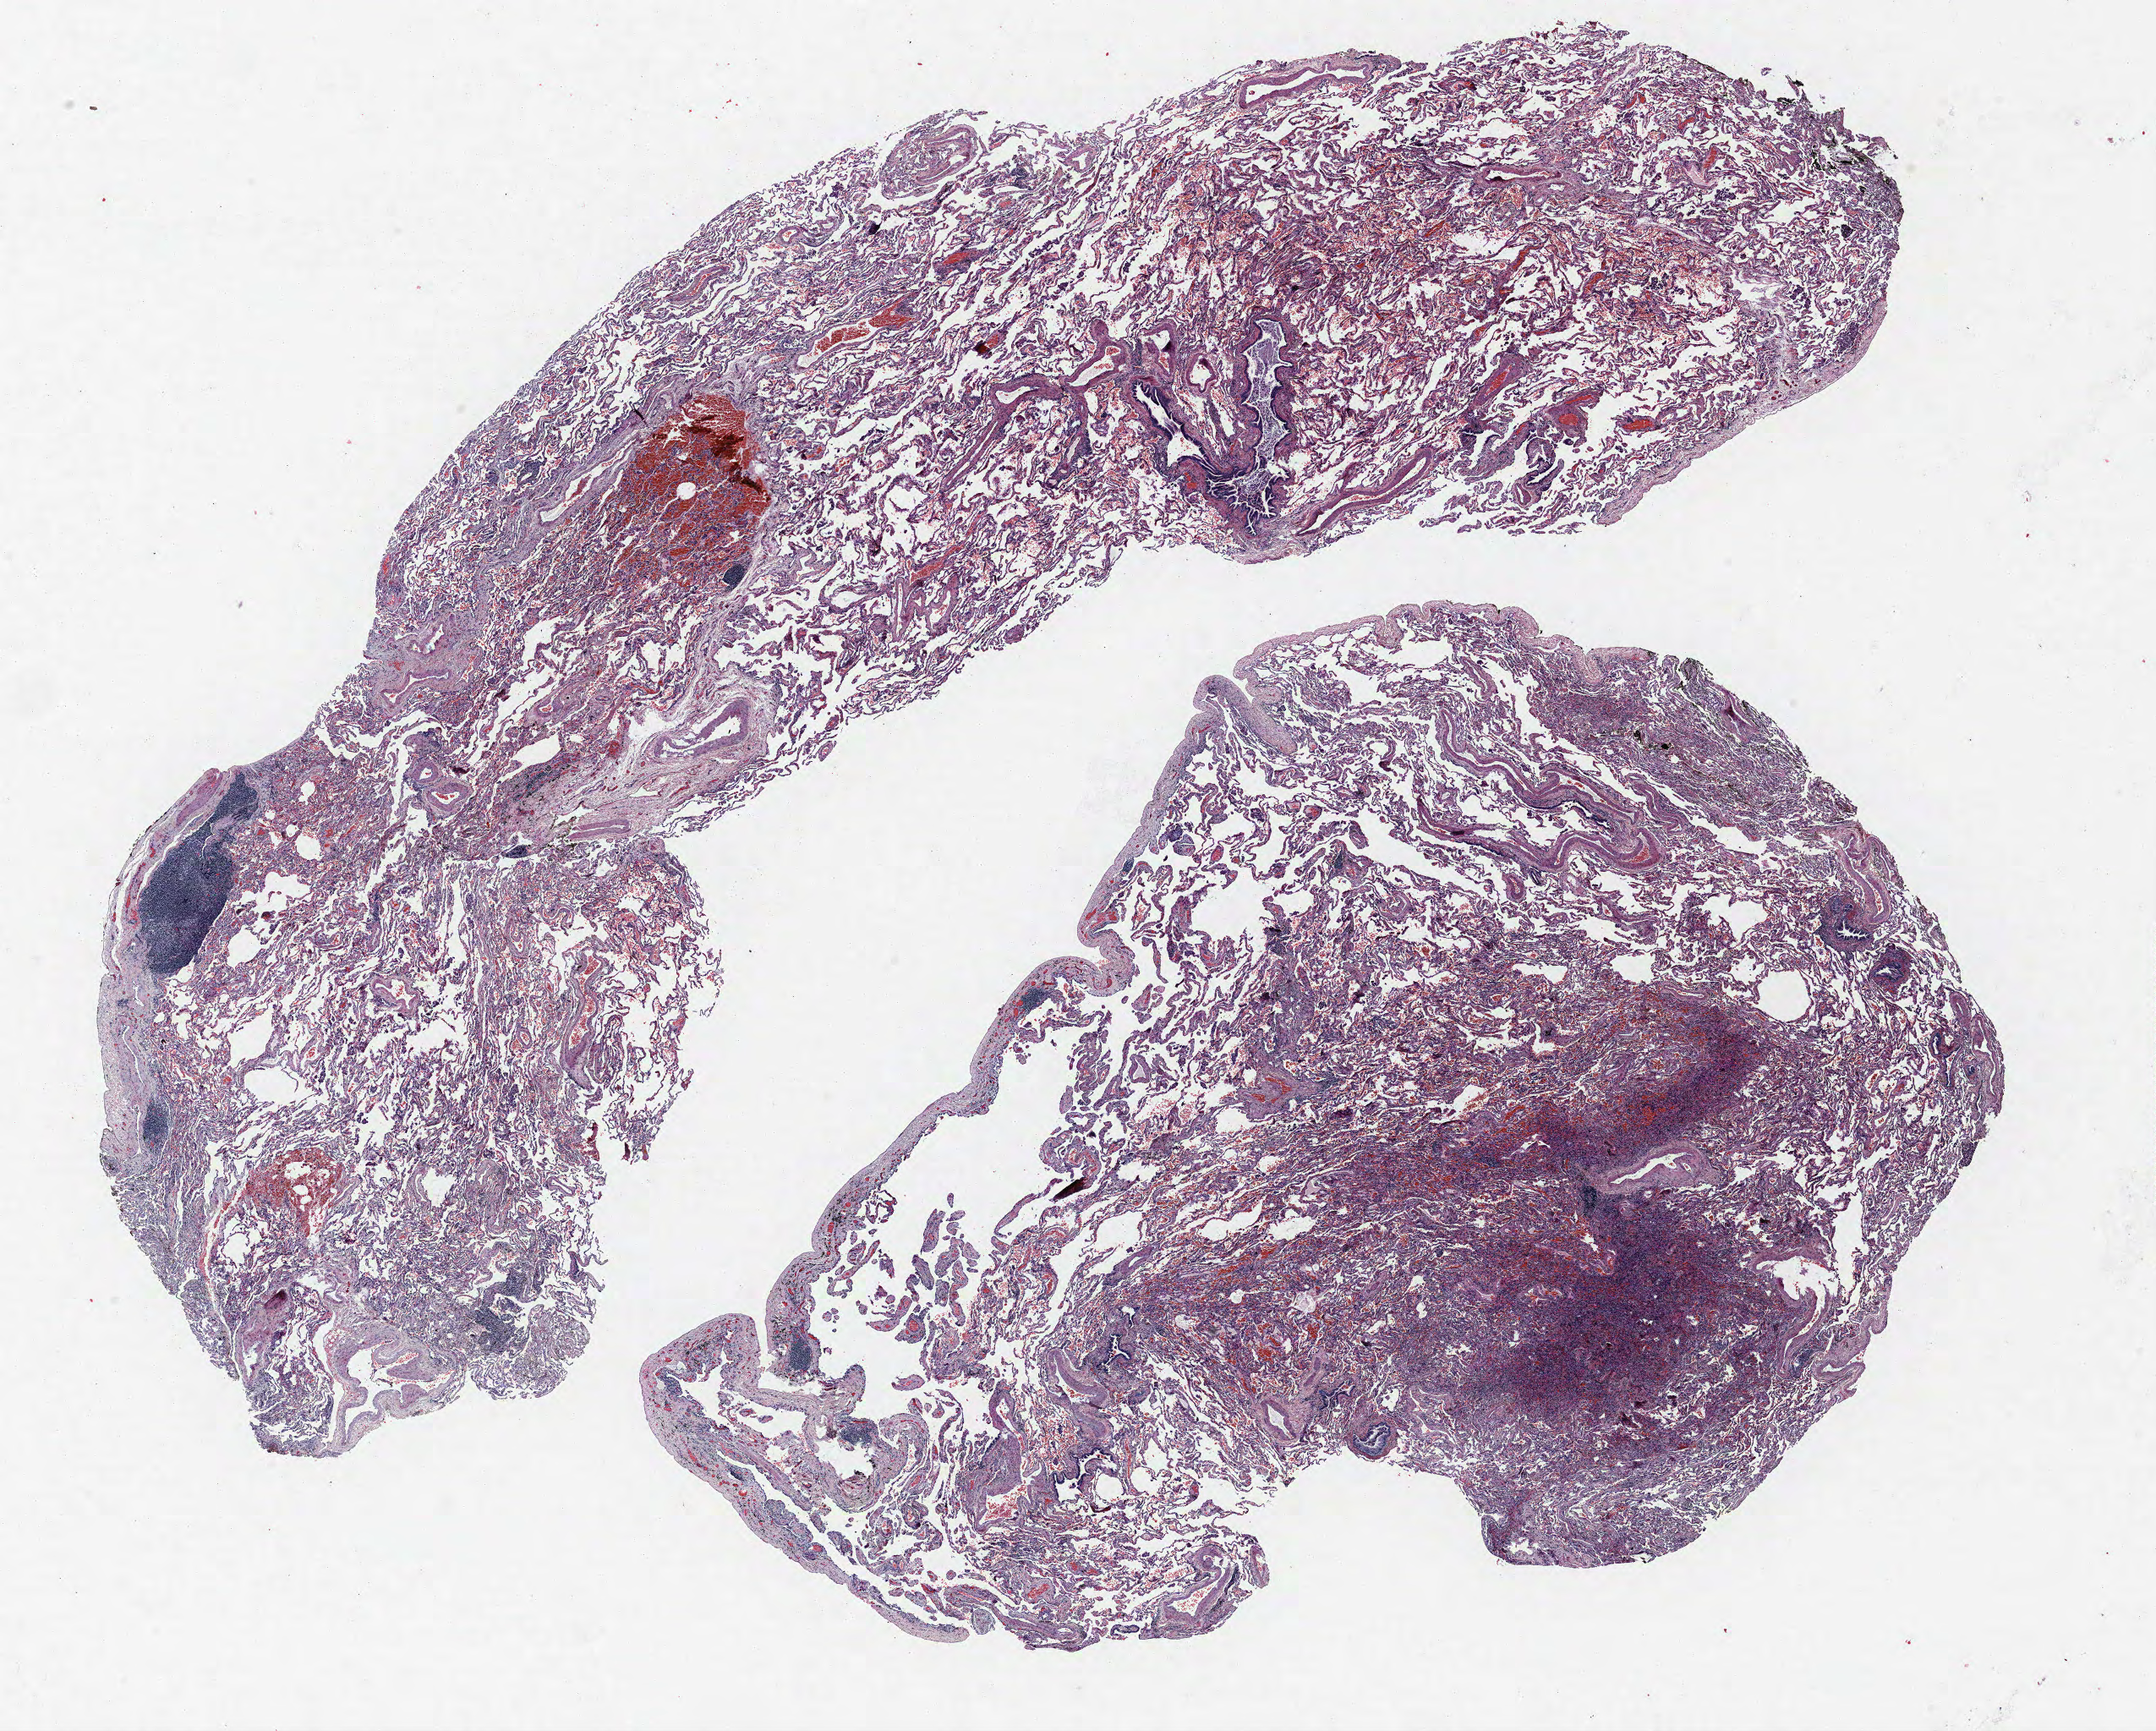
Hematoxylin and eosin (H&E) stained whole-slide image, low-resolution overview of the scanned area, about 20.4 x 16.4 mm; FFPE section; lung tissue. Male patient, aged 58 at enrolment. Former smoker at enrolment.
Participant's lung-cancer diagnosis: Squamous cell carcinoma, NOS (ICD-O-3 8070/3).